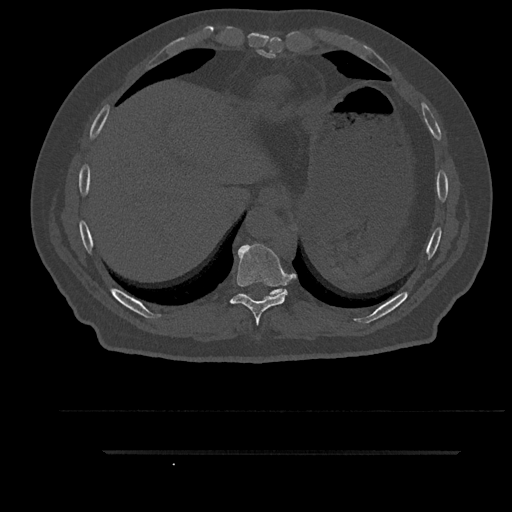
CT including the spine, one axial slice. Slice 416 of 797 in the series (ordered by position). Reconstruction kernel Br40s/3. 120 kVp. Bone window (W 1800 / L 400 HU). 512 × 512 image matrix. Male patient, age 63 years. Case-level facts recorded for this patient, not image findings: primary cancer: renal; vertebrae with lytic lesions (as recorded): T8.
Annotated regions visible in this slice (semi-automatically segmented with operator editing):
- T10 vertebra: bounding box (x1, y1, x2, y2) in pixels: (240, 289, 285, 296)
- T9 vertebra: (230, 244, 291, 325)